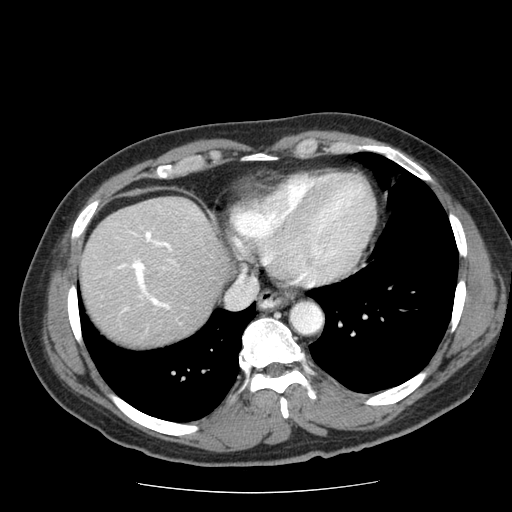
Contrast-enhanced abdominal CT (liver protocol), one axial slice. Position 62 of 85 along the scan axis. Reconstruction kernel STANDARD. Soft-tissue window (W 400 / L 40 HU). 2.5 mm slice thickness. 512 × 512 image matrix. Case-level facts recorded for this patient, not image findings: diagnosis: hepatocellular carcinoma (patient treated with transarterial chemoembolisation; whether this scan precedes or follows treatment is not stated here); TNM stage (as recorded): Stage-IIIA.
Structures marked on this image (semi-automatic segmentation, software-assisted and operator-edited):
- liver parenchyma outside the tumour (the mass and vessels are separate outlines, so this box may not span the whole liver): bounding box [x1, y1, x2, y2] px = [80, 196, 232, 344]
- liver vessels: [118, 232, 174, 311]